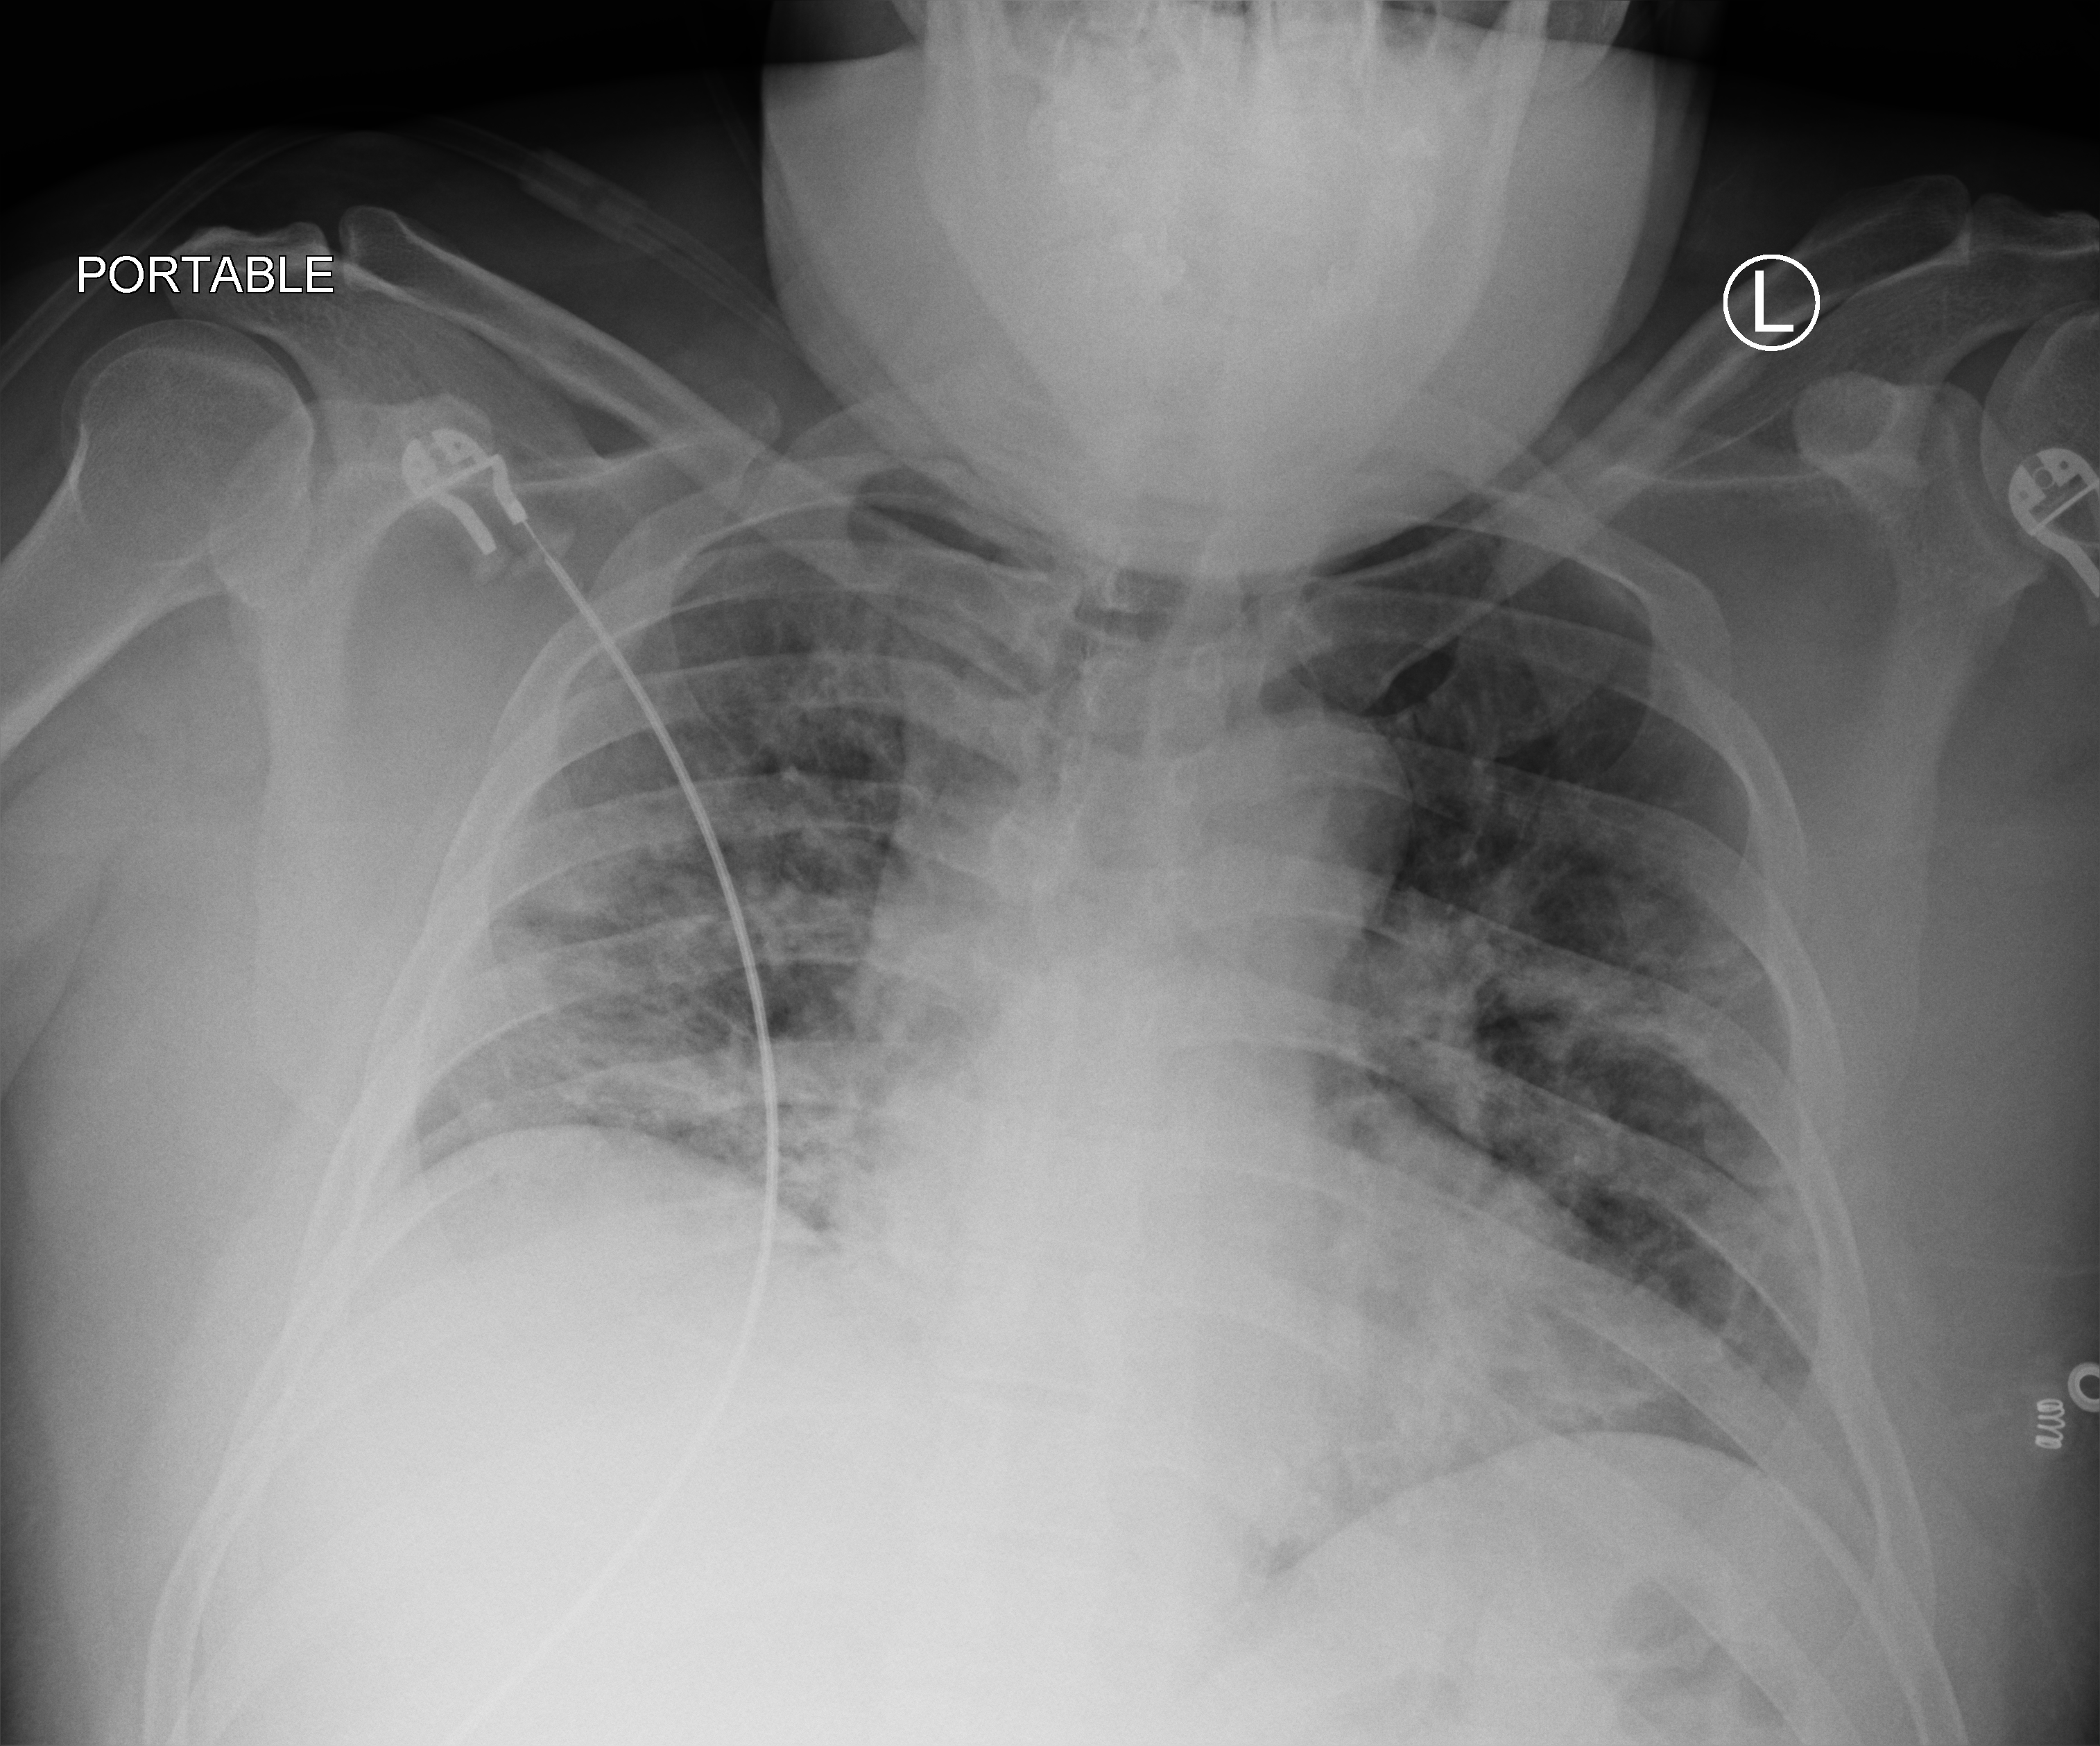
Portable chest radiograph. Male patient hospitalised with COVID-19, age 18–59 years.
Hospital-stay facts (about this admission, not read from this image; timing relative to this image not recorded): admitted to intensive care during this hospital stay: no.